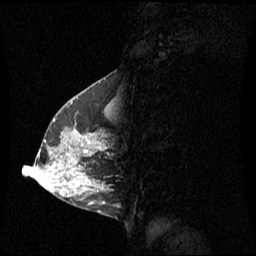
Breast MRI (dynamic contrast-enhanced), one sagittal slice. Position 24 of 60 along the scan axis. Dynamic contrast-enhanced series, image 2 of 3 at this slice position (ordered by acquisition). 1.5 T. TE 4.2 ms, TR 8.4 ms. 2 mm slice thickness. 256 × 256 image matrix, field of view 270 × 270 mm. Female patient, age 42 years. Case-level facts recorded for this patient, not image findings: setting: breast cancer imaged before/during neoadjuvant chemotherapy; receptor status: HR-positive, HER2-negative.
Outlined on this slice (semi-automatic segmentation, software-assisted and operator-edited):
- analysis volume of interest (the breast-tissue region the enhancement analysis was run in; not a lesion): box from (x=56, y=104) to (x=111, y=185) px
- tumour enhancement mask (voxels above the 70 % enhancement threshold inside the analysis volume of interest): (x=81, y=145)–(x=87, y=152)